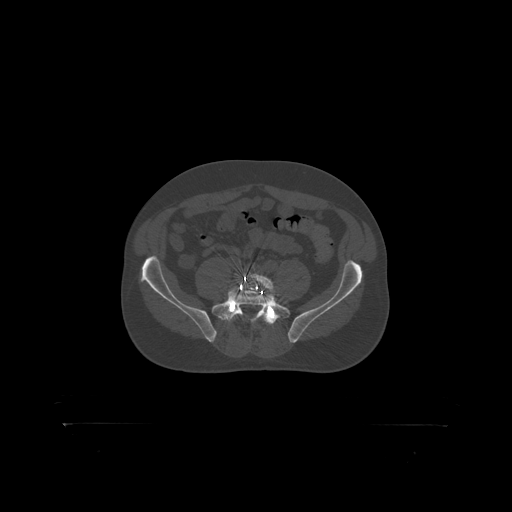
CT including the spine, one axial slice. Slice 190 of 399 in the series (ordered by position). Reconstruction kernel STANDARD. Bone window (W 1800 / L 400 HU). 1.25 mm slice thickness. 512 × 512 image matrix, field of view 650 × 650 mm. Patient: male, 46 years. From the clinical record (not read from this slice): primary cancer: skin.
Annotated regions visible in this slice (semi-automatically segmented with operator editing):
- L5 vertebra: box from (x=249, y=274) to (x=275, y=295) px